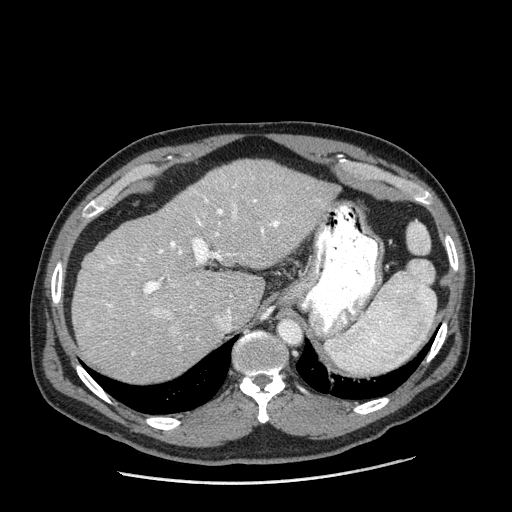
Contrast-enhanced abdominal CT (liver protocol), one axial slice. Slice 135 of 198 in the series (ordered by position). Reconstruction kernel STANDARD. 120 kVp. One of 2 acquisitions stored at this slice position. Soft-tissue window (W 400 / L 40 HU). 2.5 mm slice thickness. 512 × 512 image matrix, field of view 400 × 400 mm. From the clinical record (not read from this slice): diagnosis: hepatocellular carcinoma (patient treated with transarterial chemoembolisation; whether this scan precedes or follows treatment is not stated here); TNM stage (as recorded): Stage-II; Child-Pugh class: A.
Outlined on this slice (semi-automatically segmented with operator editing):
- liver parenchyma outside the tumour (the mass and vessels are separate outlines, so this box may not span the whole liver): bounding box [x1, y1, x2, y2] px = [72, 160, 337, 382]
- liver vessels: [88, 177, 279, 355]